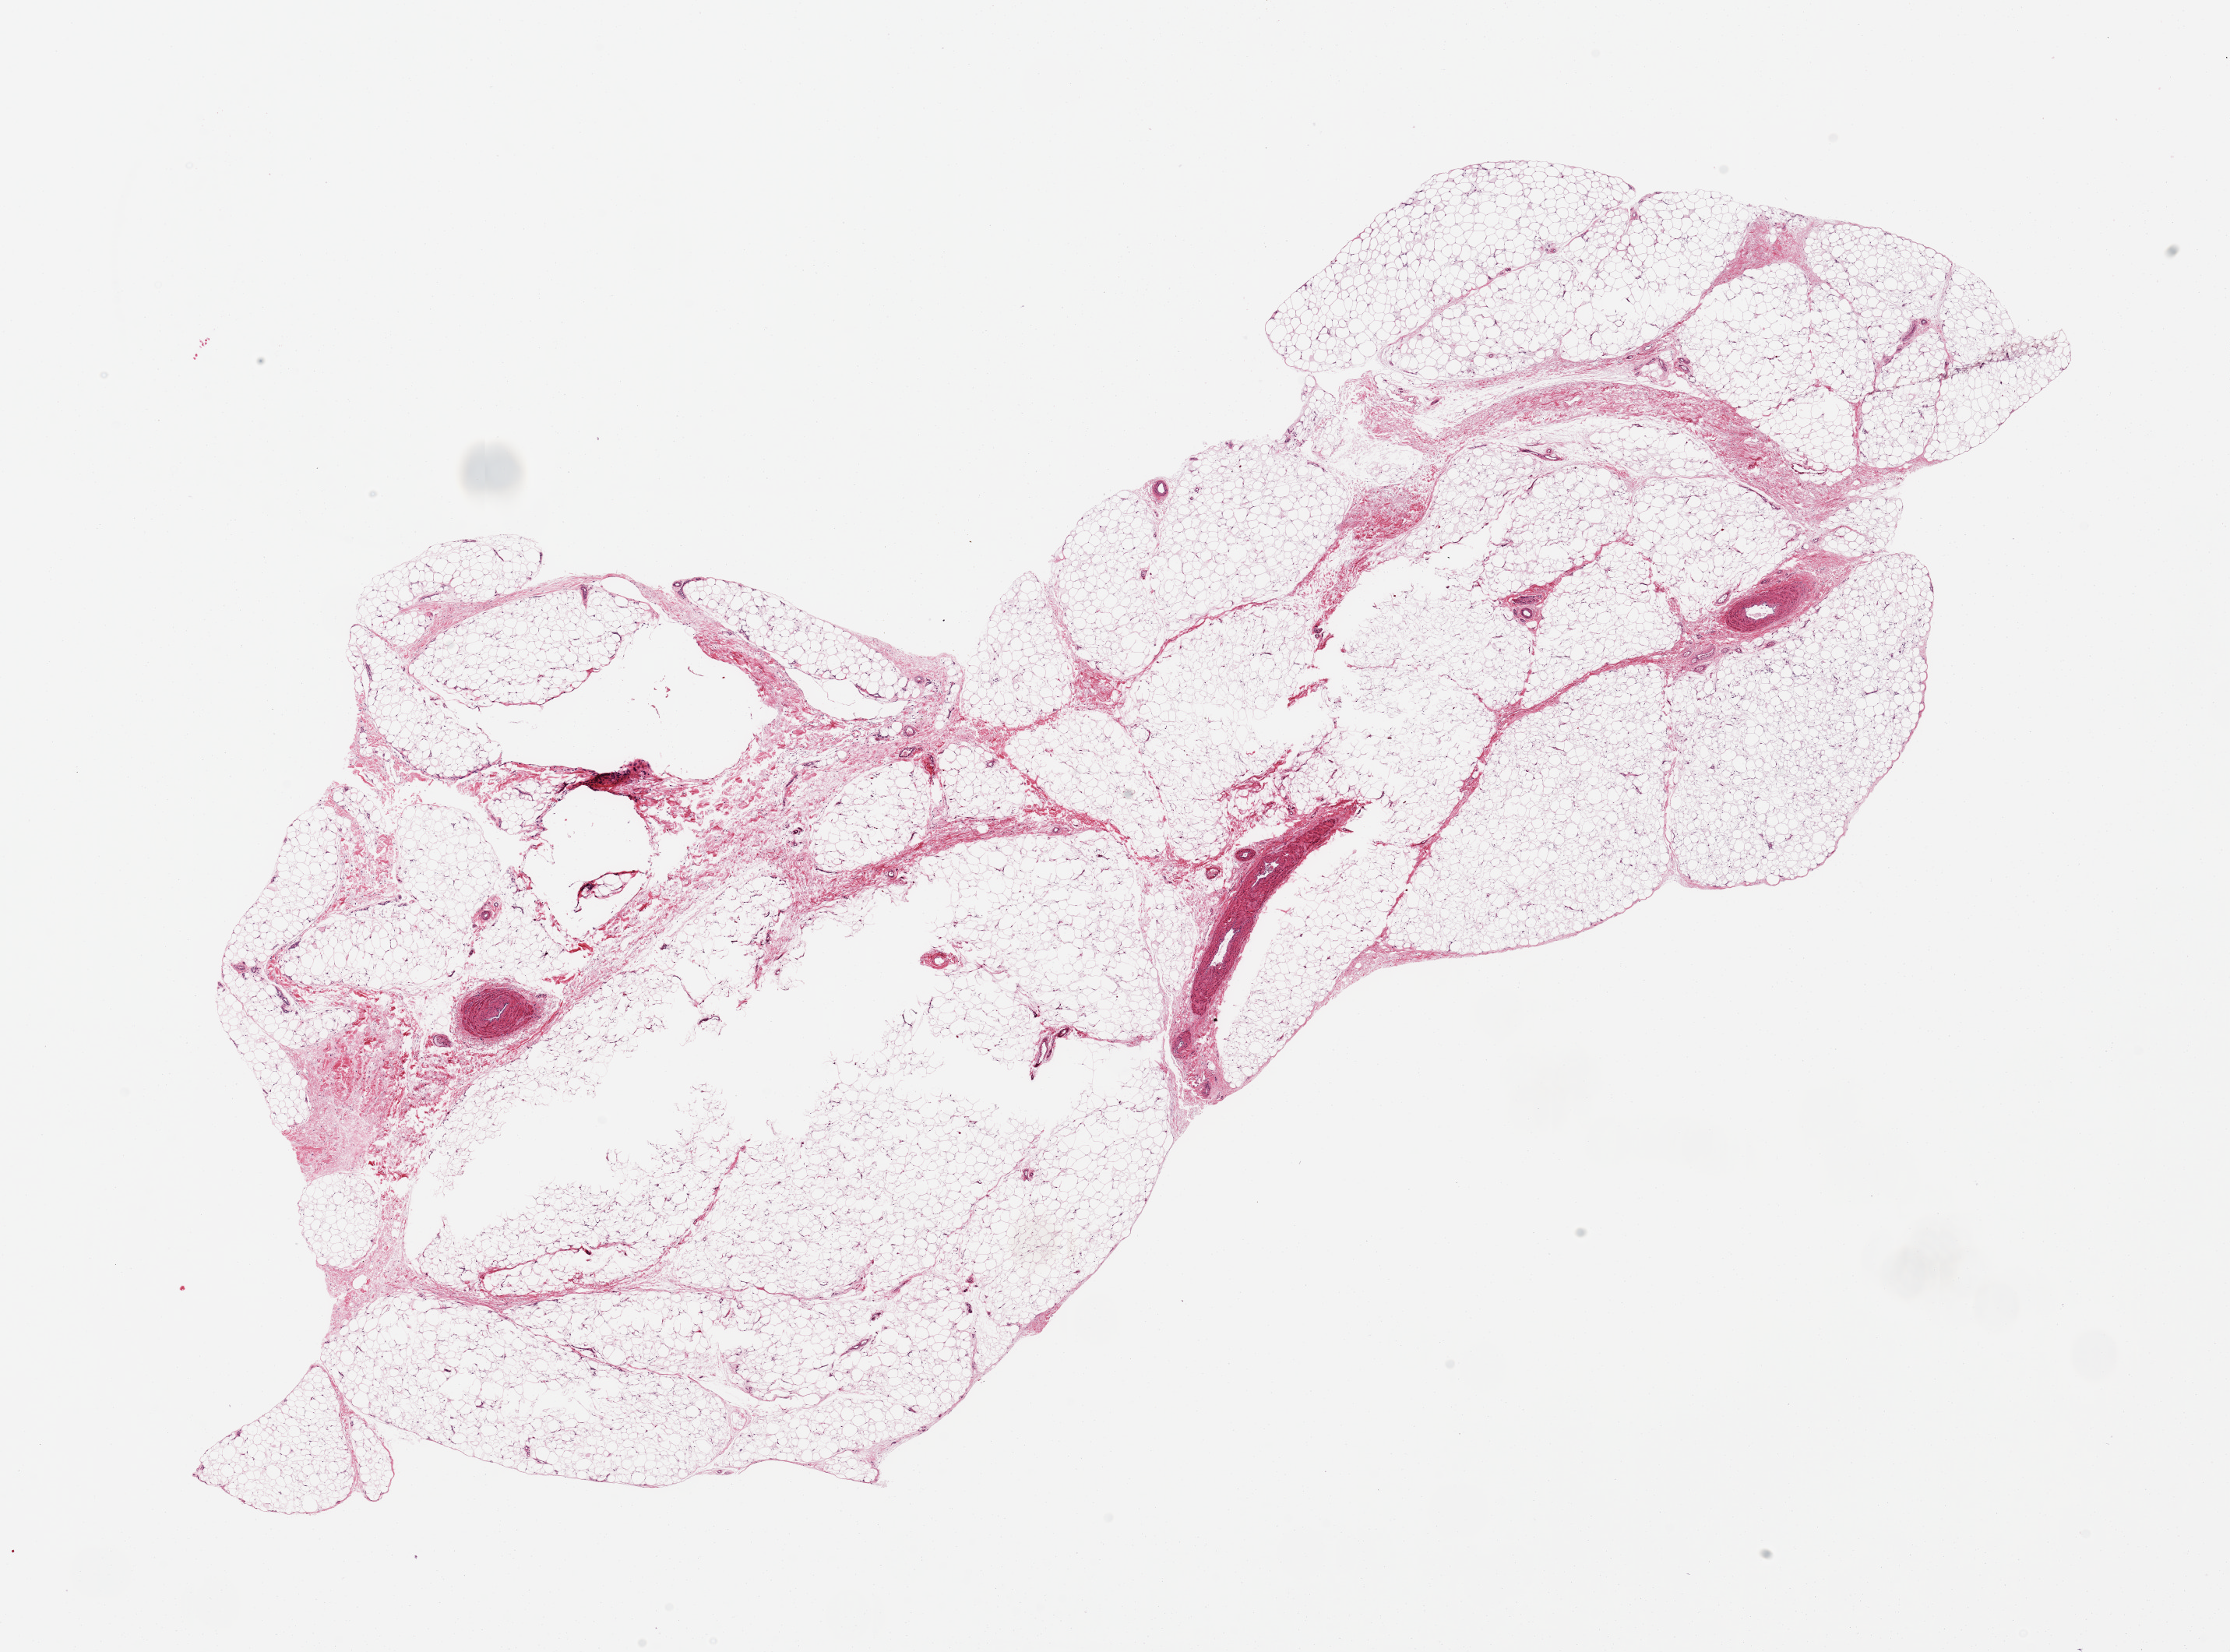
Whole-slide image, haematoxylin and eosin stain, brightfield, a low-resolution overview of the entire scanned area, about 22.6 x 16.8 mm (from a 20x scan), PAXgene-fixed, paraffin-embedded tissue, sampled site (target tissue): adipose tissue, donor tissue sample. Donor sex: male.
- reviewer comment on this tissue sample: 19x5mm with 6x1mm central hole tear of under-fixation